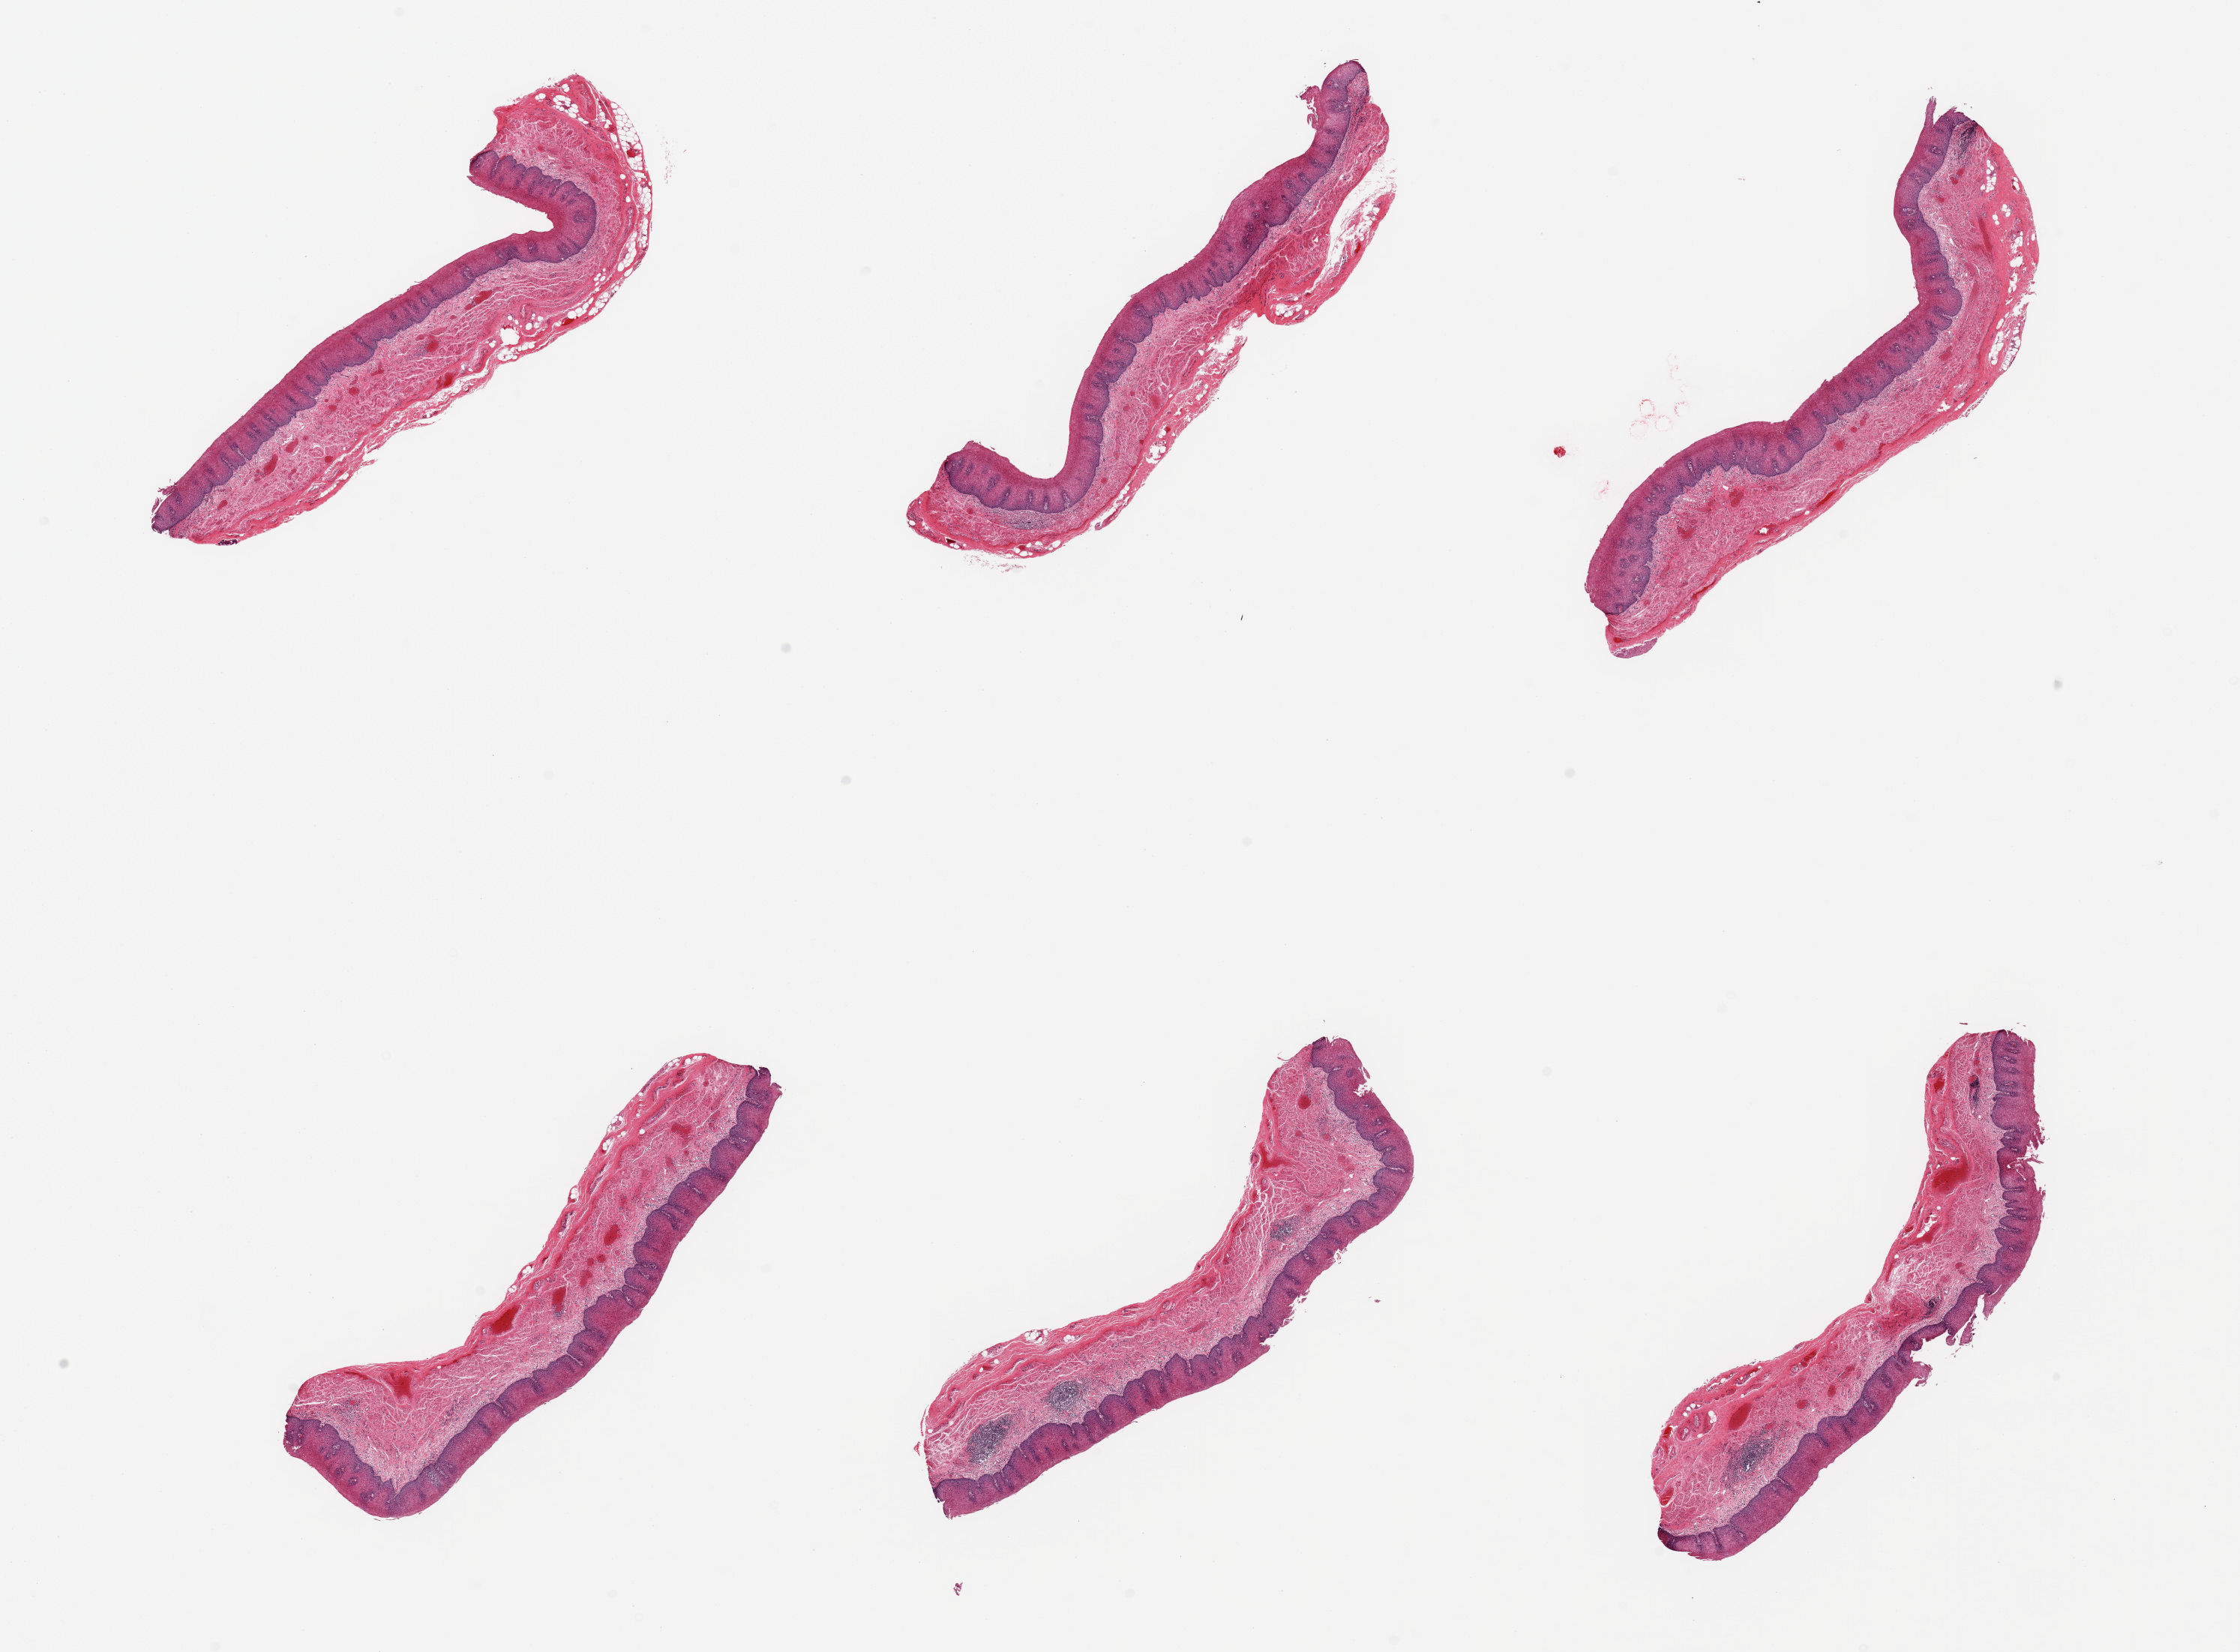
Hematoxylin and eosin (H&E) whole-slide image — whole scanned area (about 23.6 x 17.4 mm, from a 20x scan) shown as a low-resolution overview. PAXgene-fixed paraffin-embedded (PFPE) section. Section of esophageal mucous membrane (target tissue). Donor tissue sample. Donor sex: male.
• review note (as recorded): 6 pieces; congestion and few lymphocytic aggregates